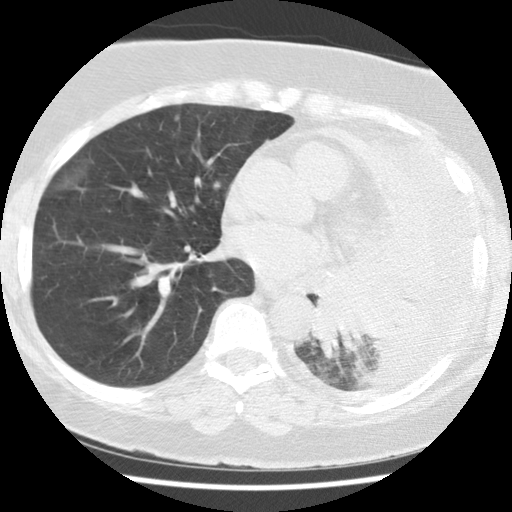
Low-dose screening chest CT, axial slice, baseline screening round, lung window (W 1500 / L -600 HU), 2.5 mm slice thickness, standard (soft-tissue) reconstruction kernel (STANDARD), slice 63 of 114 in the series. Female, age 65 years at enrolment. Current smoker at enrolment.
- Expert reader's lesion annotation, box from (x=306, y=282) to (x=417, y=373) px.
- Screening reader's record for this exam (one nodule recorded; not confirmed to be the boxed lesion): non-calcified nodule or mass ≥4 mm, left lower lobe, 74 × 48 mm, spiculated (stellate) margins, soft tissue attenuation.
- Official screen result: positive, change unspecified: nodule(s) >= 4 mm or enlarging nodule(s), mass(es), or other non-specific abnormalities suspicious for lung cancer.